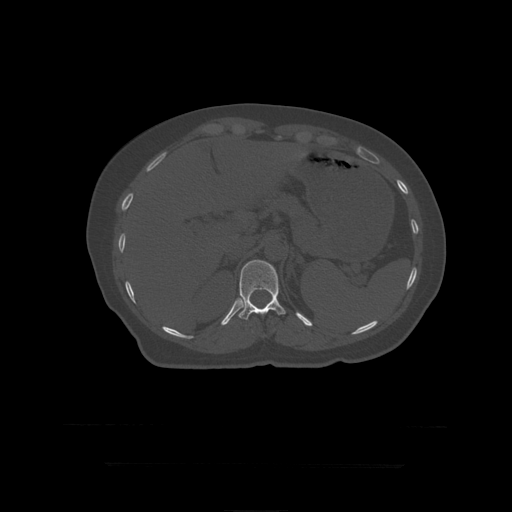
CT including the spine, one axial slice. Position 200 of 399 along the scan axis. Reconstruction kernel STANDARD. Bone window (W 1800 / L 400 HU). 1.25 mm slice thickness. 512 × 512 image matrix, field of view 450 × 450 mm. Patient age 41 years. From the clinical record (not read from this slice): primary cancer: breast.
Structures marked on this image (semi-automatic segmentation, software-assisted and operator-edited):
- T12 vertebra: bounding box [x1, y1, x2, y2] px = [238, 260, 286, 320]